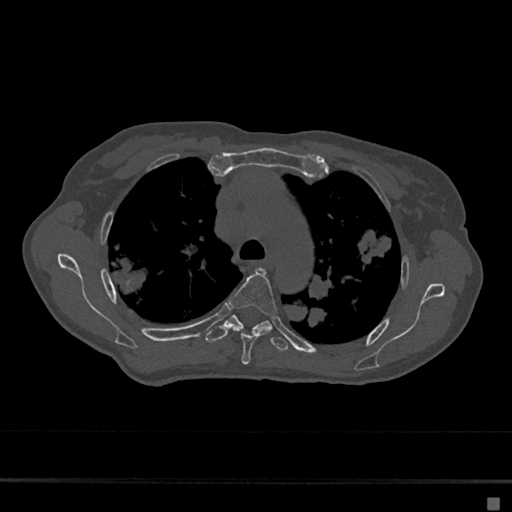
CT including the spine, one axial slice. Position 487 of 797 along the scan axis. Reconstruction kernel Br40s/3. Bone window (W 1800 / L 400 HU). 0.5 mm slice thickness. 512 × 512 image matrix. Patient: female, 68 years. Case-level facts recorded for this patient, not image findings: primary cancer: renal.
Outlined on this slice (semi-automatically segmented with operator editing):
- T4 vertebra: bounding box [x1, y1, x2, y2] px = [228, 268, 277, 365]
- T5 vertebra: [205, 315, 288, 351]